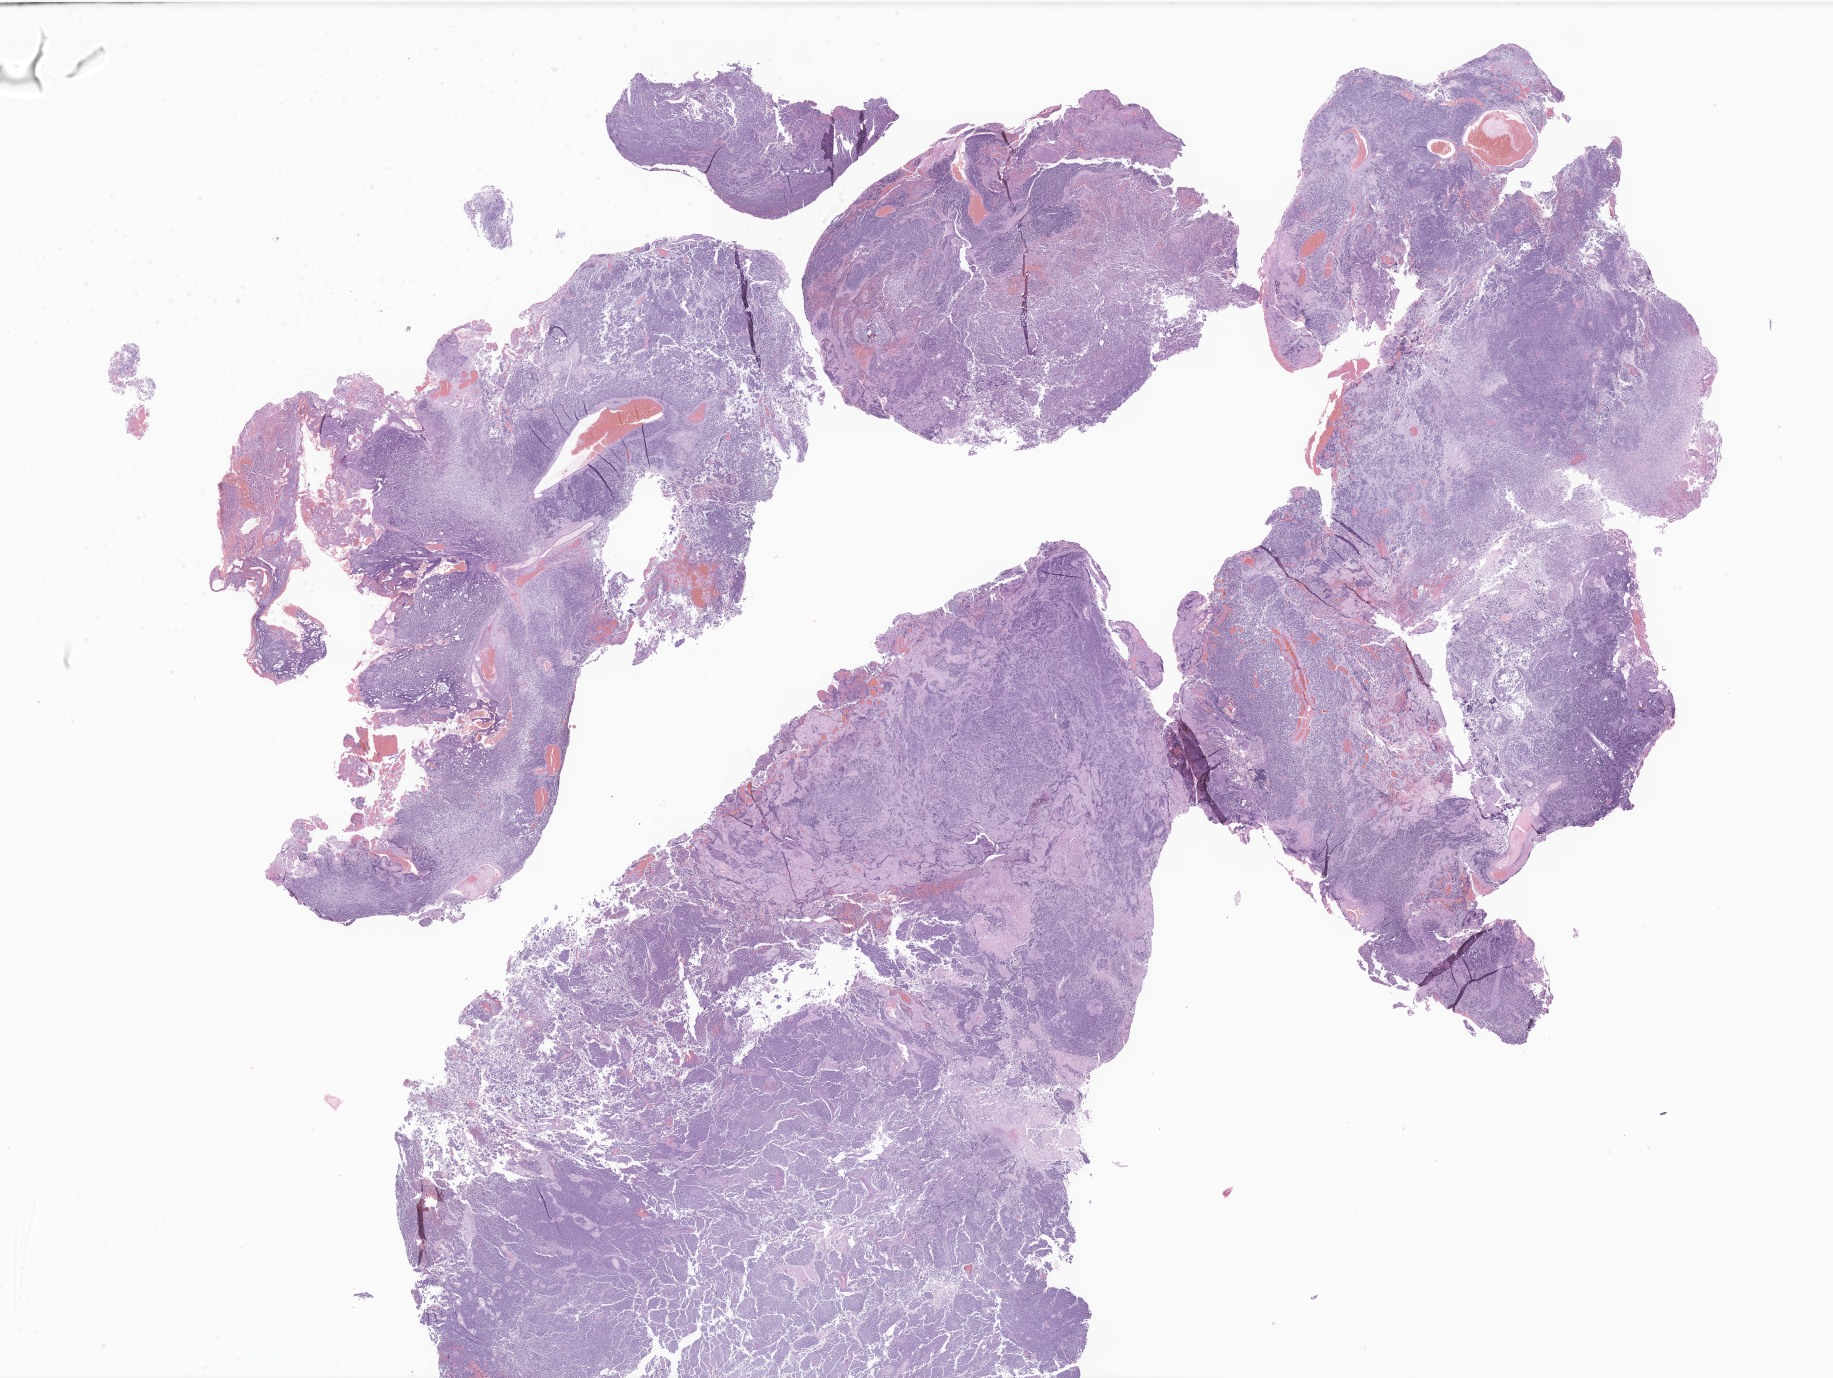
Digitized hematoxylin and eosin (H&E)-stained section of tumor tissue from the brain — shown as a low-resolution overview of the whole scanned area (about 30.9 x 23.2 mm). Formalin-fixed, paraffin-embedded (FFPE) tissue. Patient: male, age 103 months (8 years 7 months).
• diagnosis: Medulloblastoma, NOS